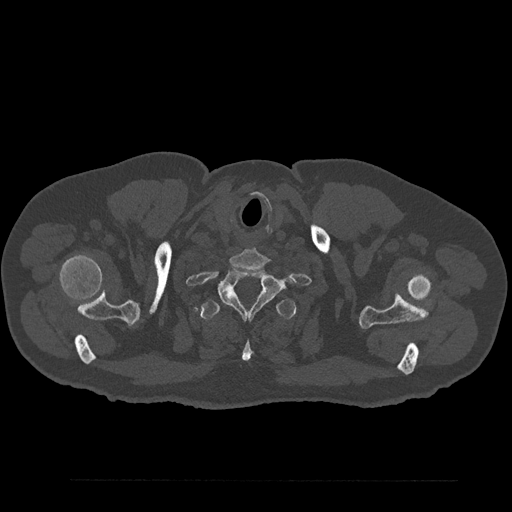
CT including the spine, one axial slice; position 747 of 797 along the scan axis; reconstruction kernel Br40s/3; 120 kVp; bone window (W 1800 / L 400 HU); 0.5 mm slice thickness; 512 × 512 image matrix. Male patient, age 61 years. Case-level facts recorded for this patient, not image findings: primary cancer: prostate.
Outlined on this slice (semi-automatically segmented with operator editing):
- T1 vertebra: bounding box (x1, y1, x2, y2) in pixels: (218, 268, 292, 319)
- T2 vertebra: (200, 298, 296, 362)